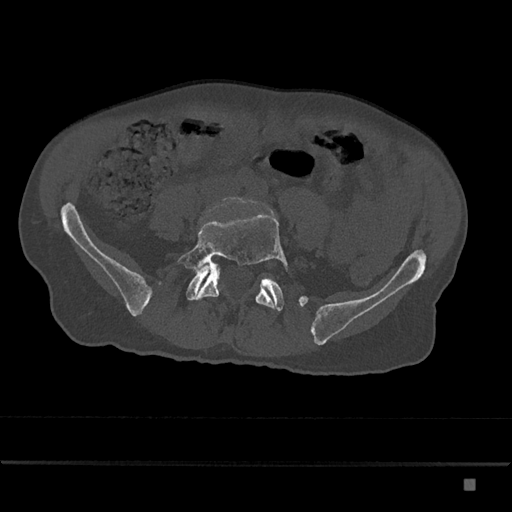
CT including the spine, one axial slice. Slice 272 of 797 in the series (ordered by position). 120 kVp. Bone window (W 1800 / L 400 HU). 512 × 512 image matrix, field of view 390 × 390 mm. Patient: male, 72 years. From the clinical record (not read from this slice): primary cancer: prostate.
Structures marked on this image (semi-automatically segmented with operator editing):
- L5 vertebra: box from (x=177, y=213) to (x=288, y=309) px